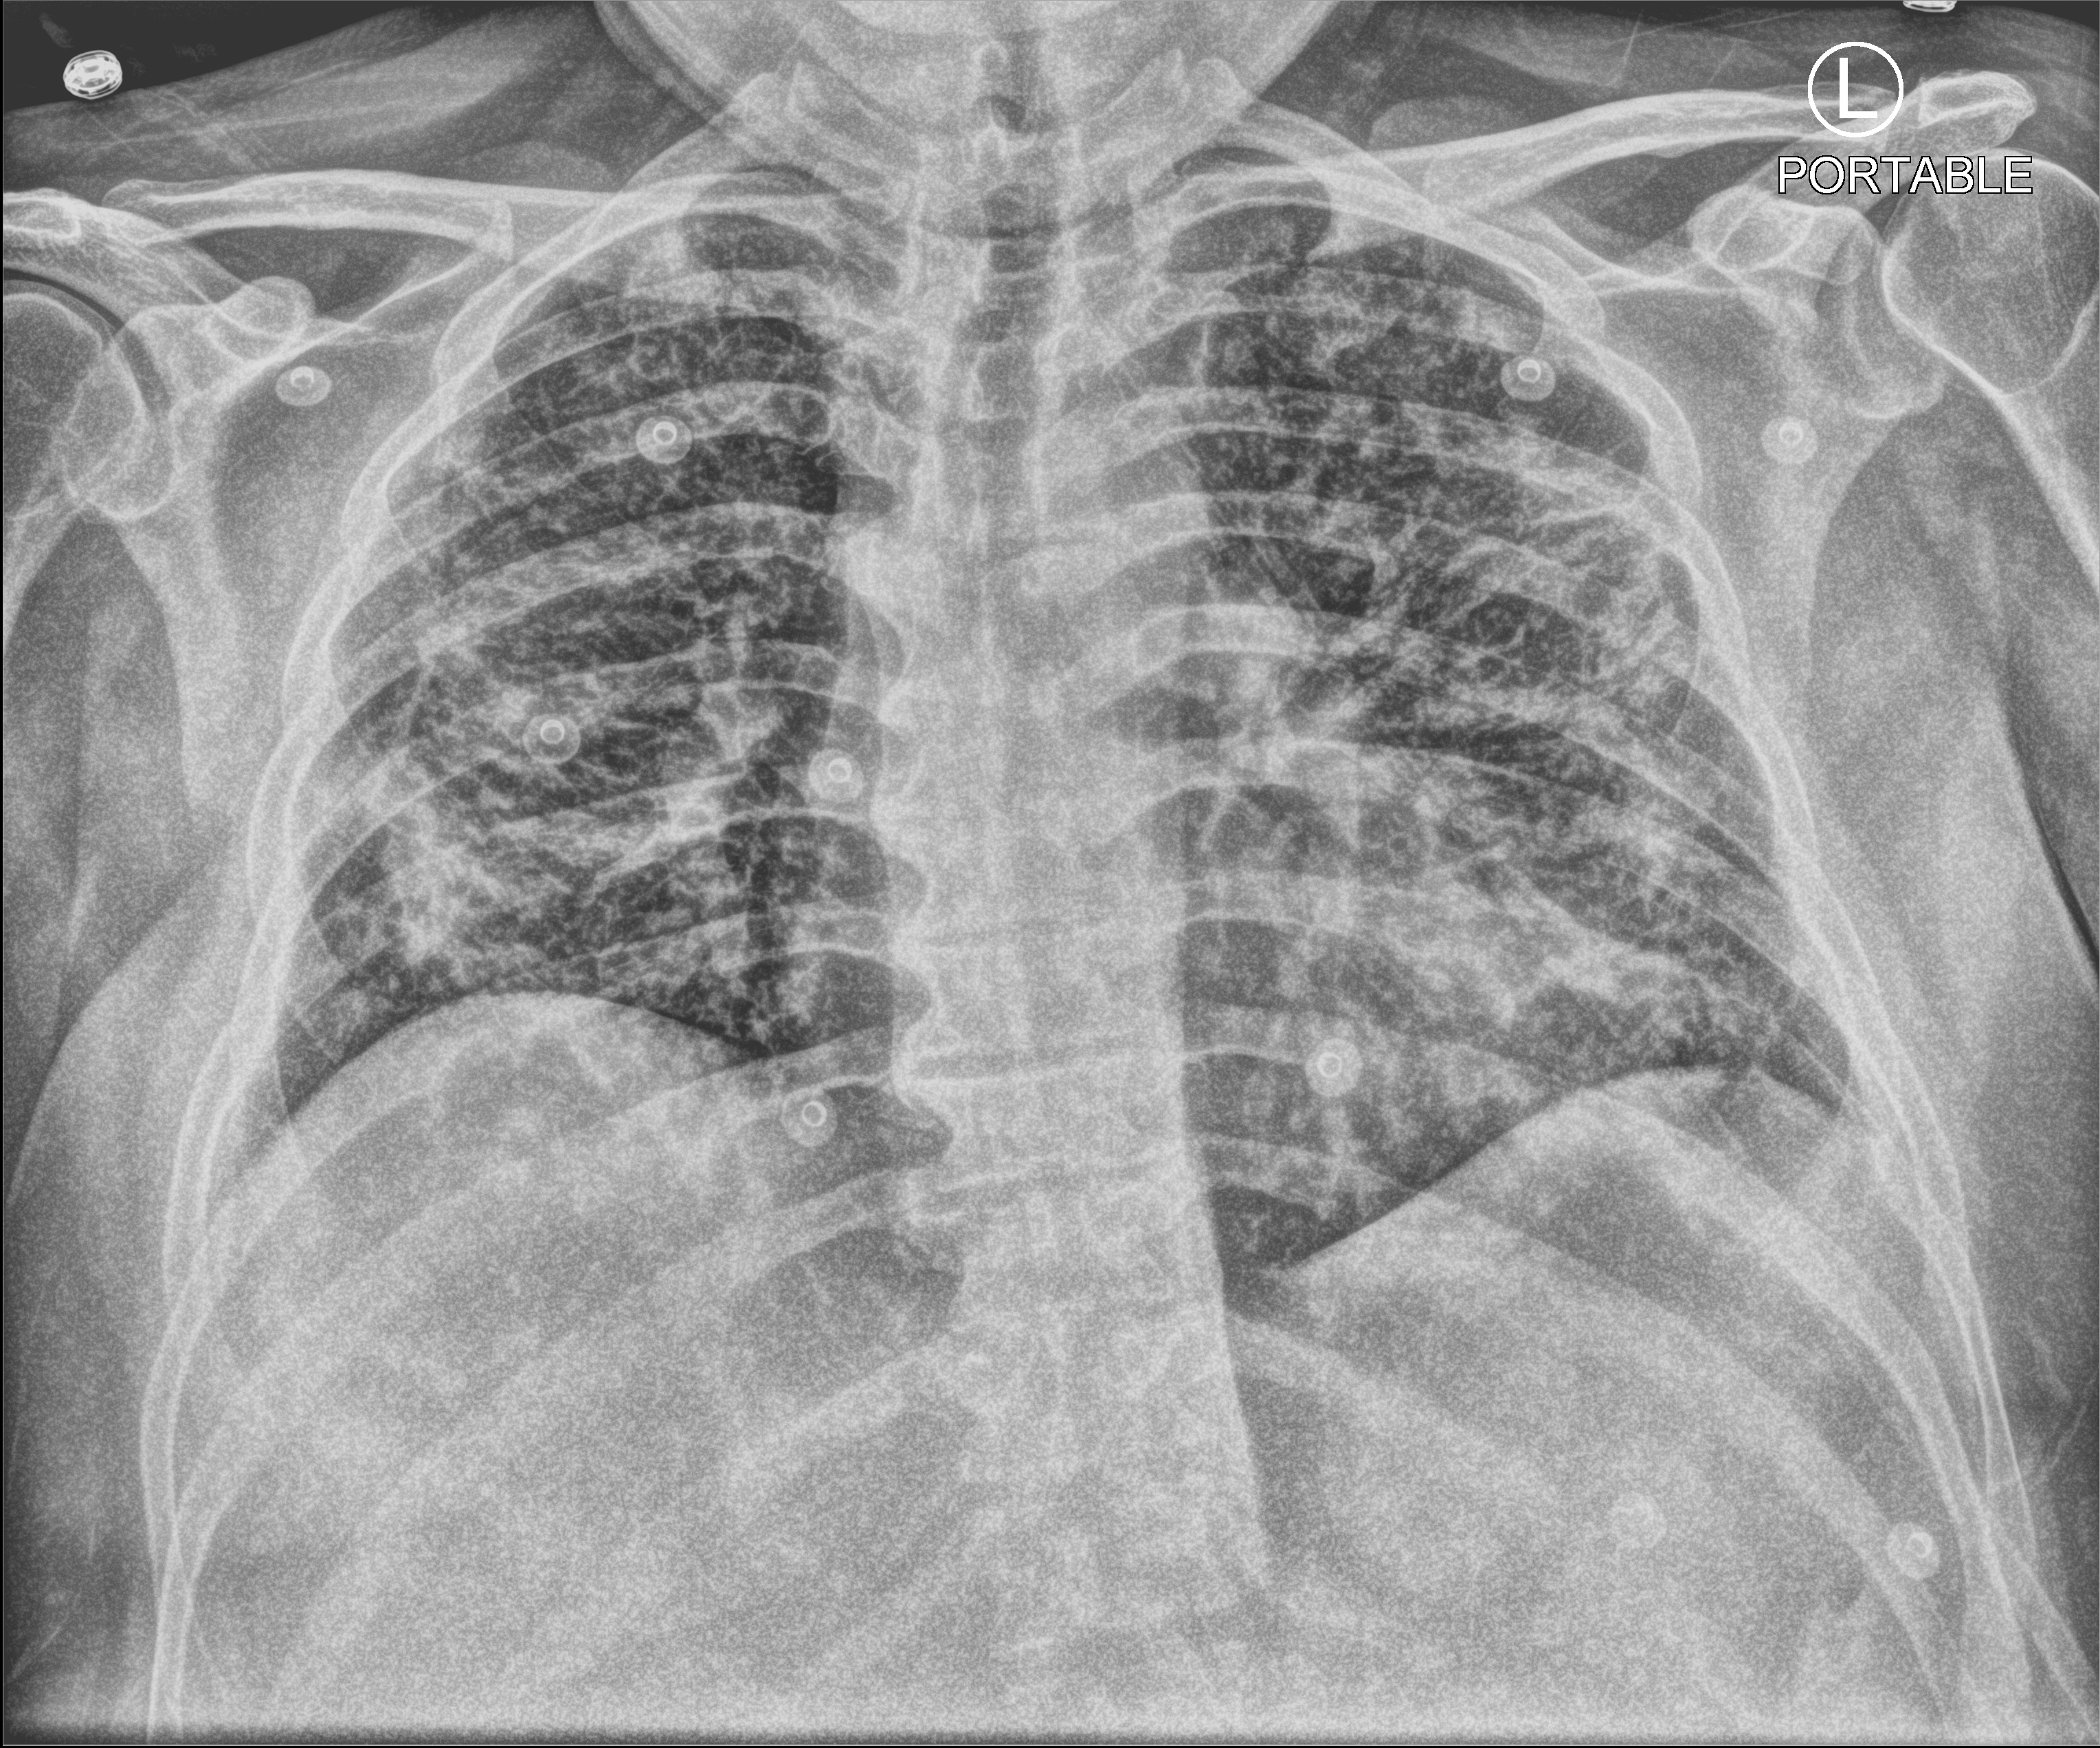
Portable chest radiograph, anteroposterior (AP) projection. Patient hospitalised with COVID-19; male, aged 18–59 years.
Hospital-stay facts (about this admission, not read from this image; timing relative to this image not recorded):
- admitted to intensive care during this hospital stay: yes
- length of hospital stay: 24 days
- COPD (admission record): no